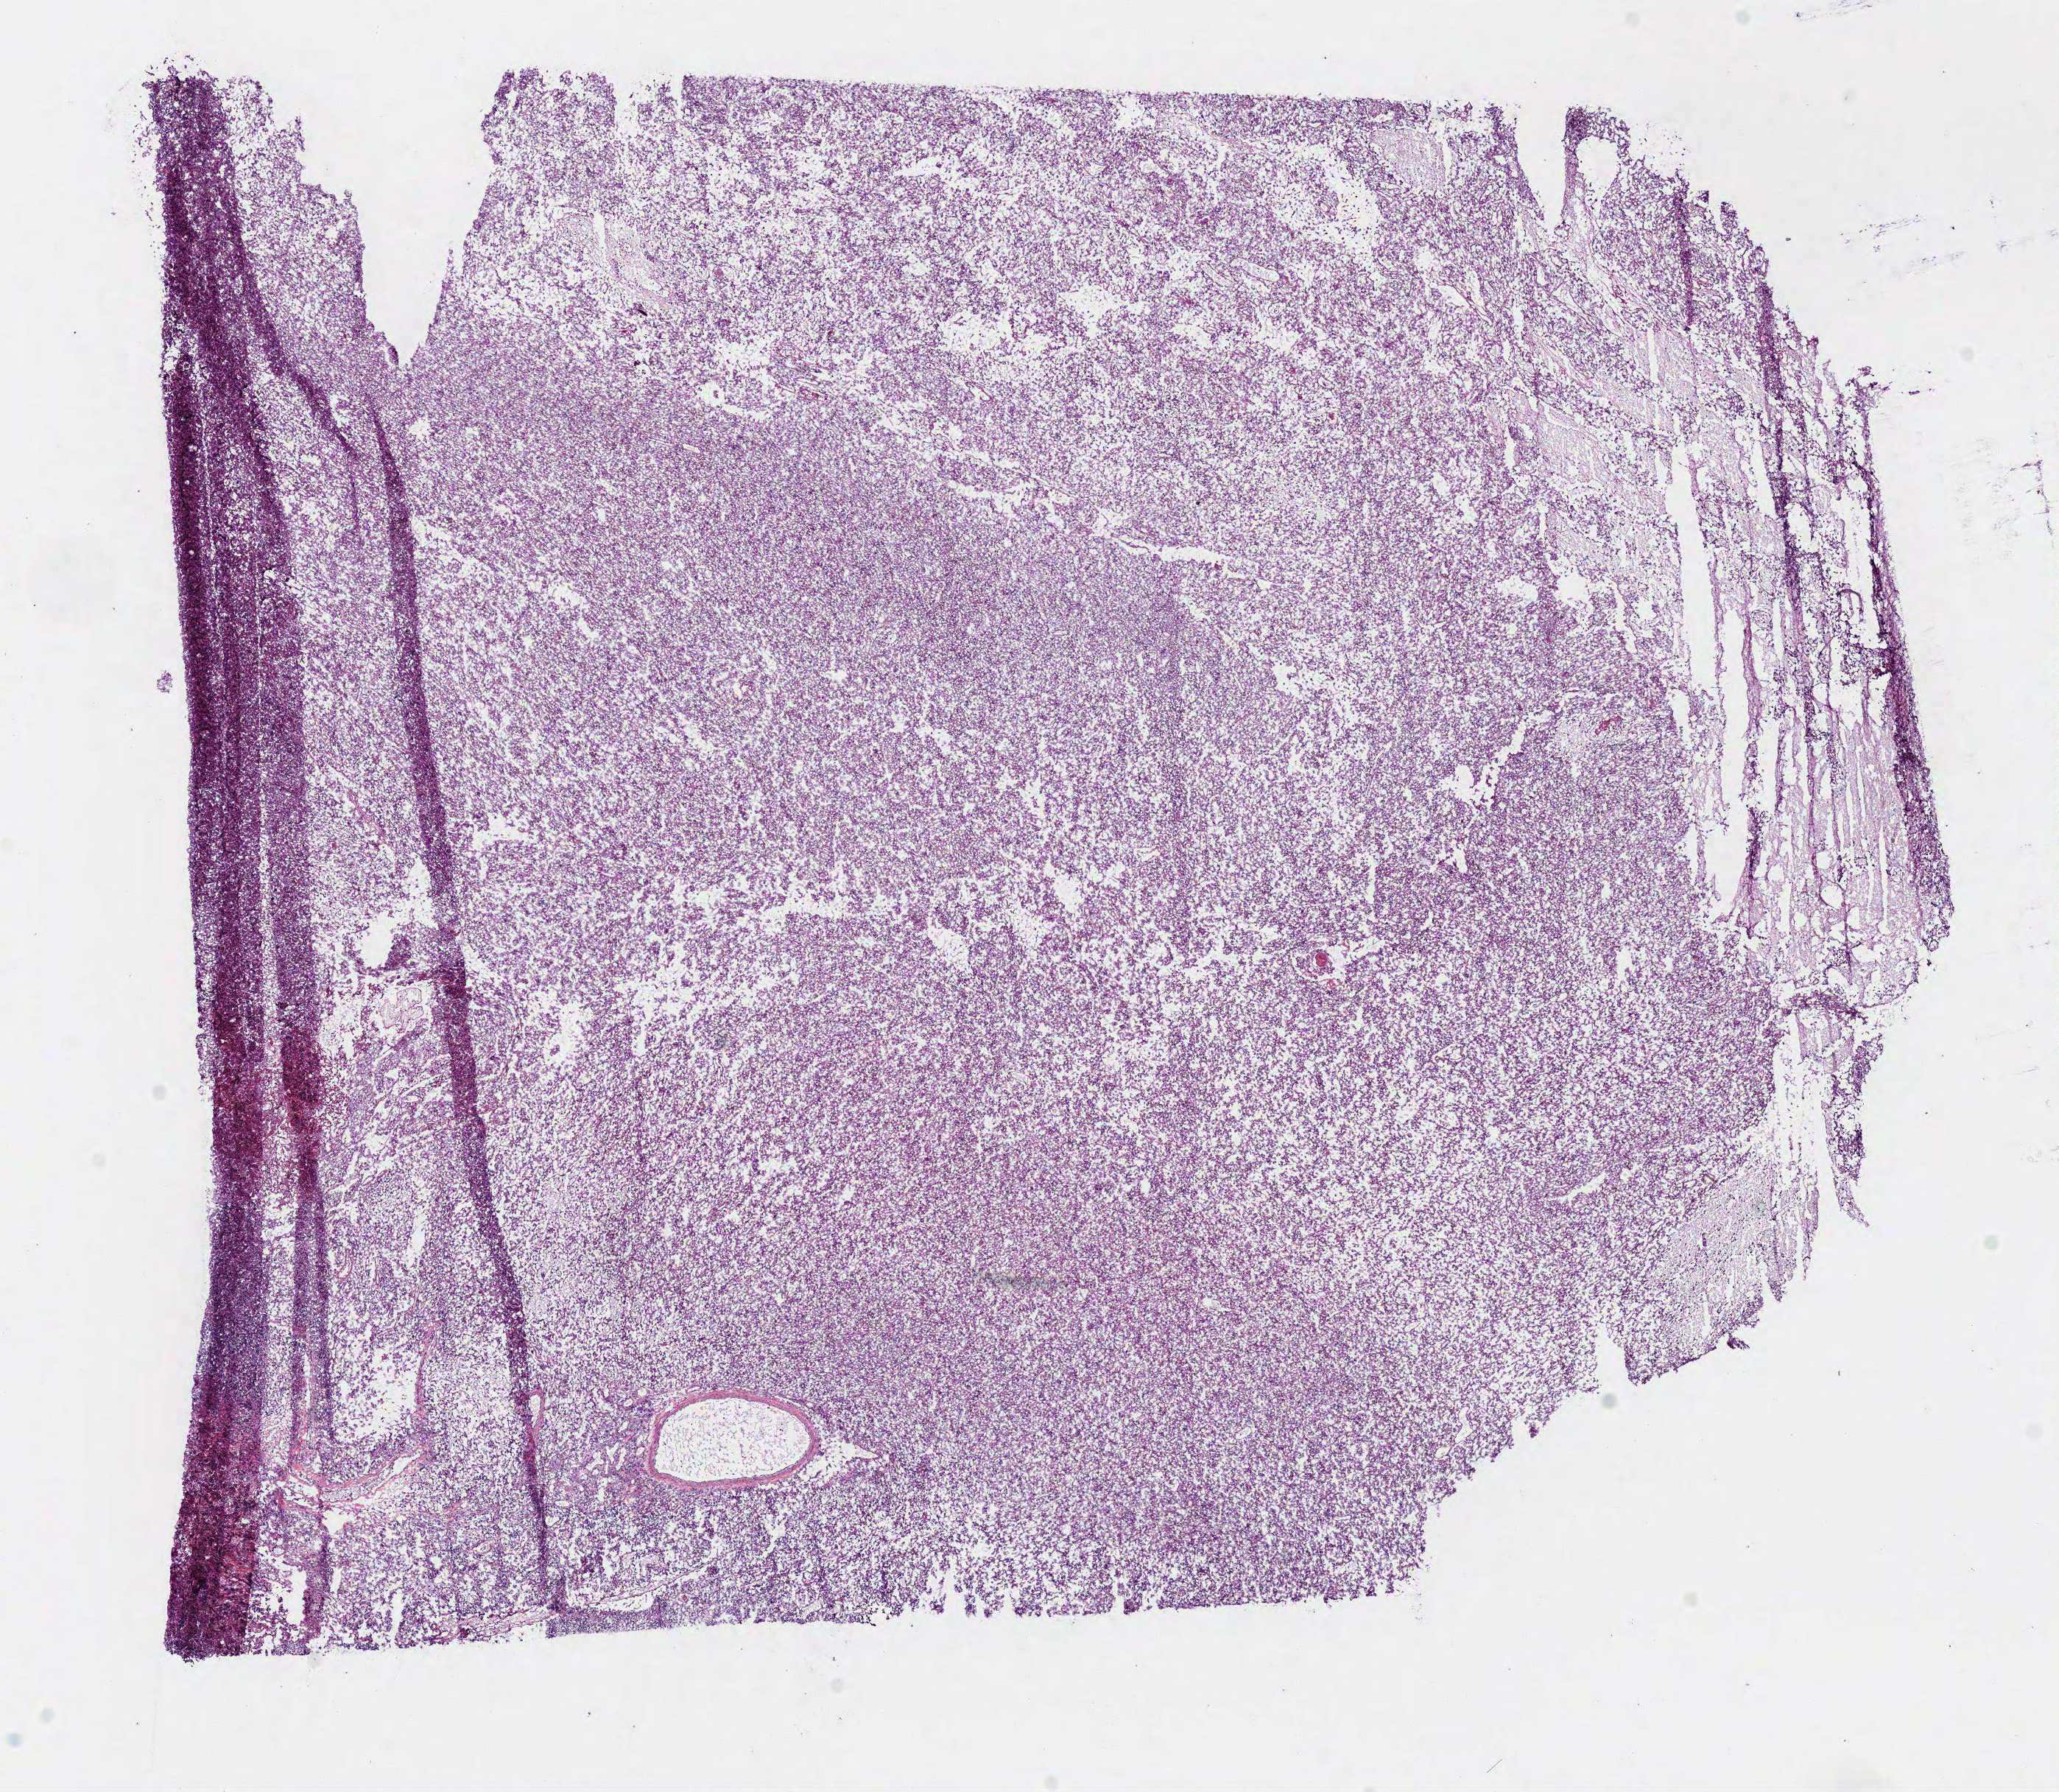
Whole-slide histology image, H&E — shown as a low-resolution overview of the whole scanned area (about 11.0 x 9.6 mm, slide scanned at 40x); frozen section; brain, primary tumour sample. Patient: male, age at initial diagnosis 56 years. Composition of this section per pathologist review: tumour cells 100%, tumour nuclei 65%, normal cells 0%, stromal cells 0%, necrosis 0%.
Diagnosis: Glioblastoma.